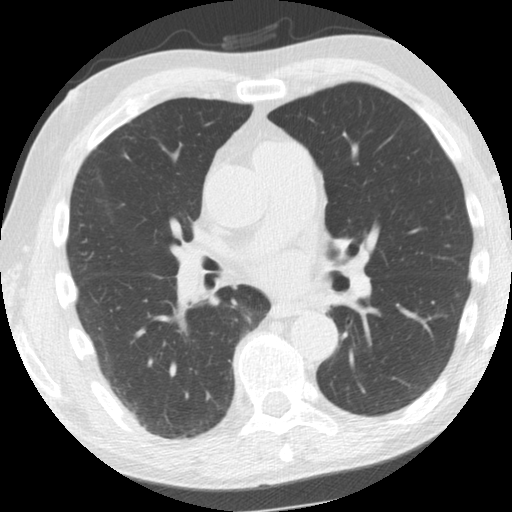
Axial slice from a low-dose chest CT screening exam. Second annual screen. Lung window (W 1500 / L -600 HU). Slice 76 of 156 in the series. Male participant, aged 61 years at enrolment. Former smoker at enrolment.
Expert-annotated lung lesion, bounding box (x1, y1, x2, y2) in pixels: (297, 291, 347, 330). Screening reader's record for this exam: no non-calcified nodule ≥4 mm recorded. Official screen result: negative screen, minor abnormalities not suspicious for lung cancer. Later outcome: lung cancer diagnosed 775 days after this screen — squamous cell carcinoma, NOS, left upper lobe, left lower lobe, well differentiated (G1), stage IIB (AJCC 6th edition), 100 mm at pathology.